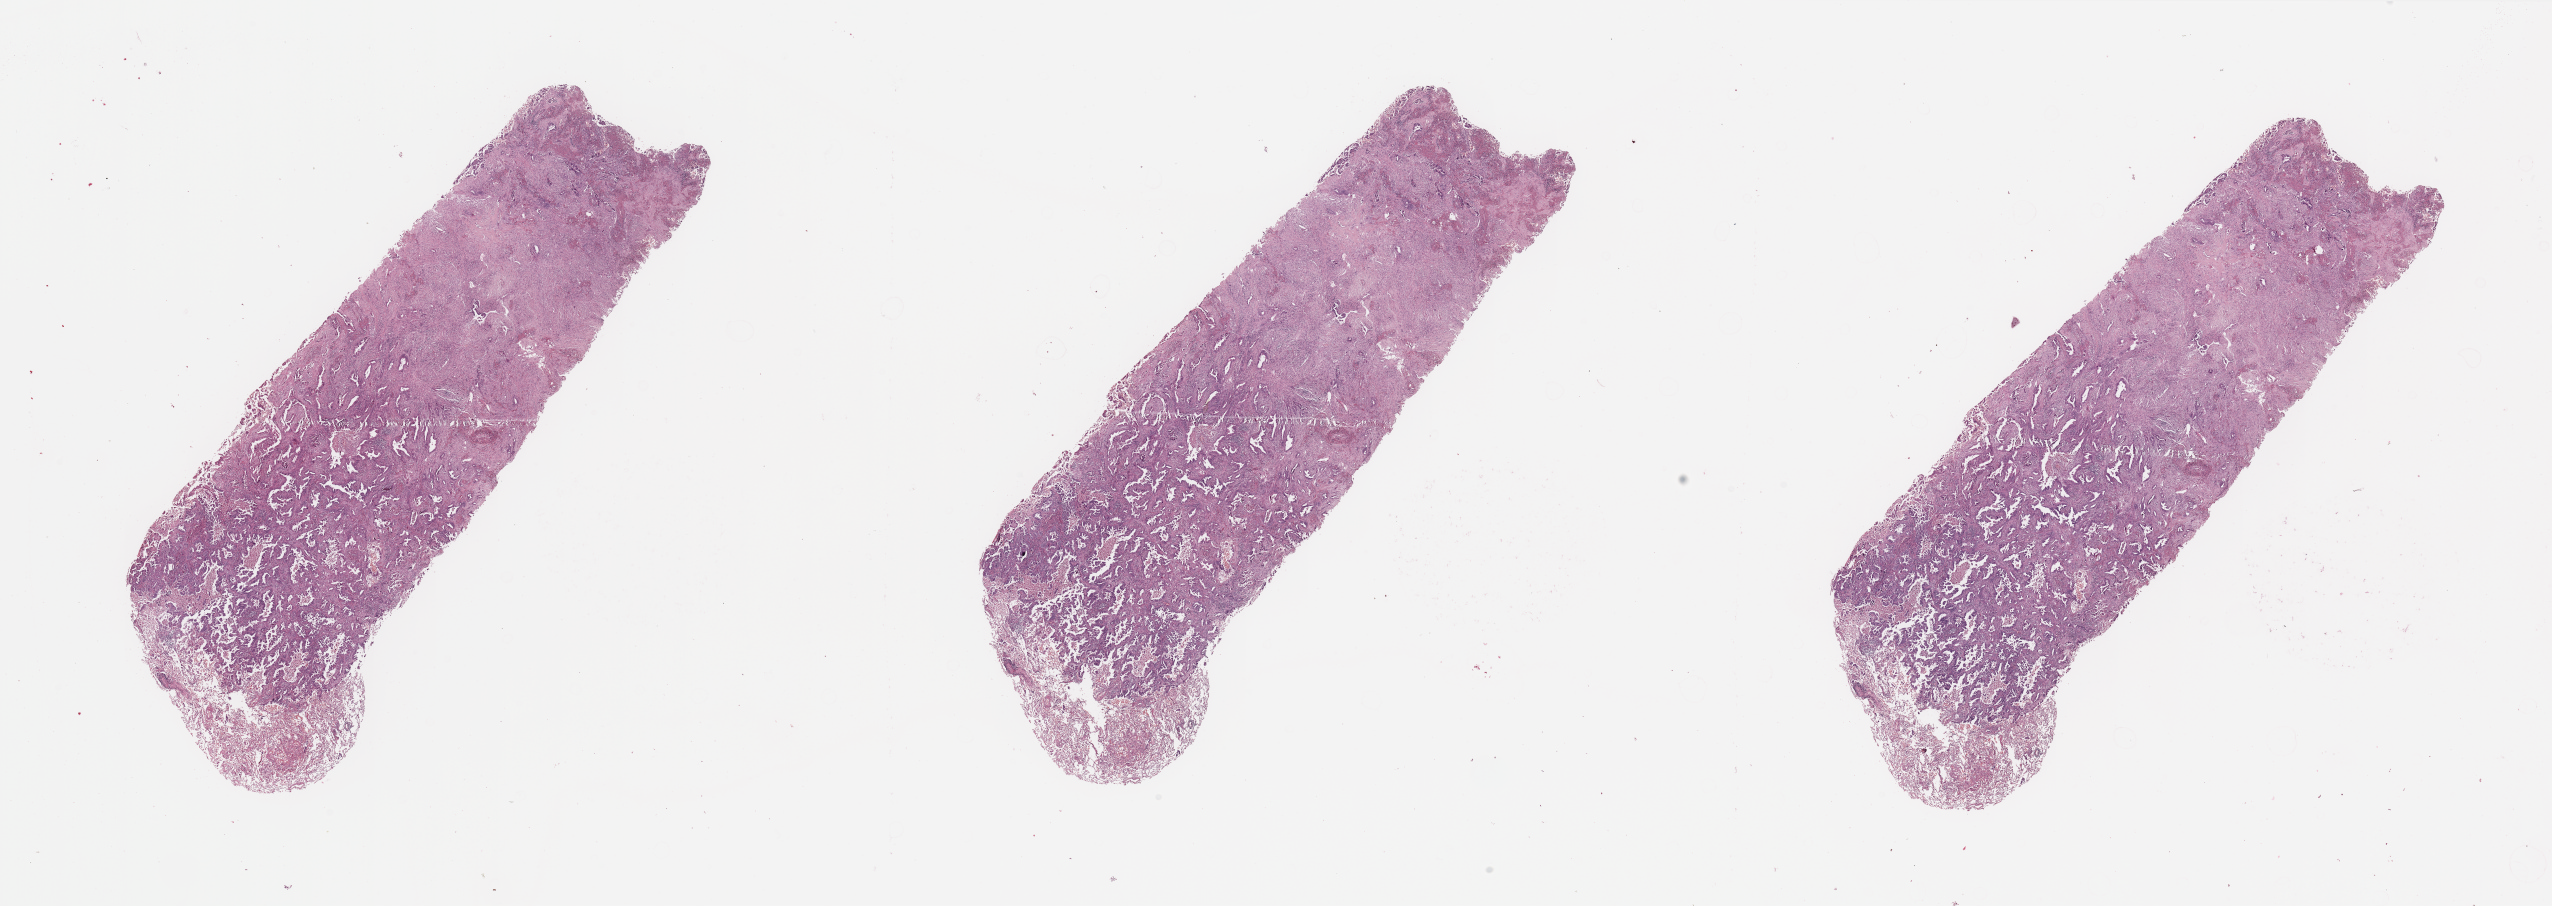
Hematoxylin and eosin (H&E) stained whole-slide image — low-resolution overview of the scanned area, about 40.4 x 14.3 mm, lung, tumour tissue. Patient: female, age 73 years. Histologic grade: G2 (moderately differentiated).
• diagnosis: Adenocarcinoma, NOS
• AJCC pathologic stage: IIIA